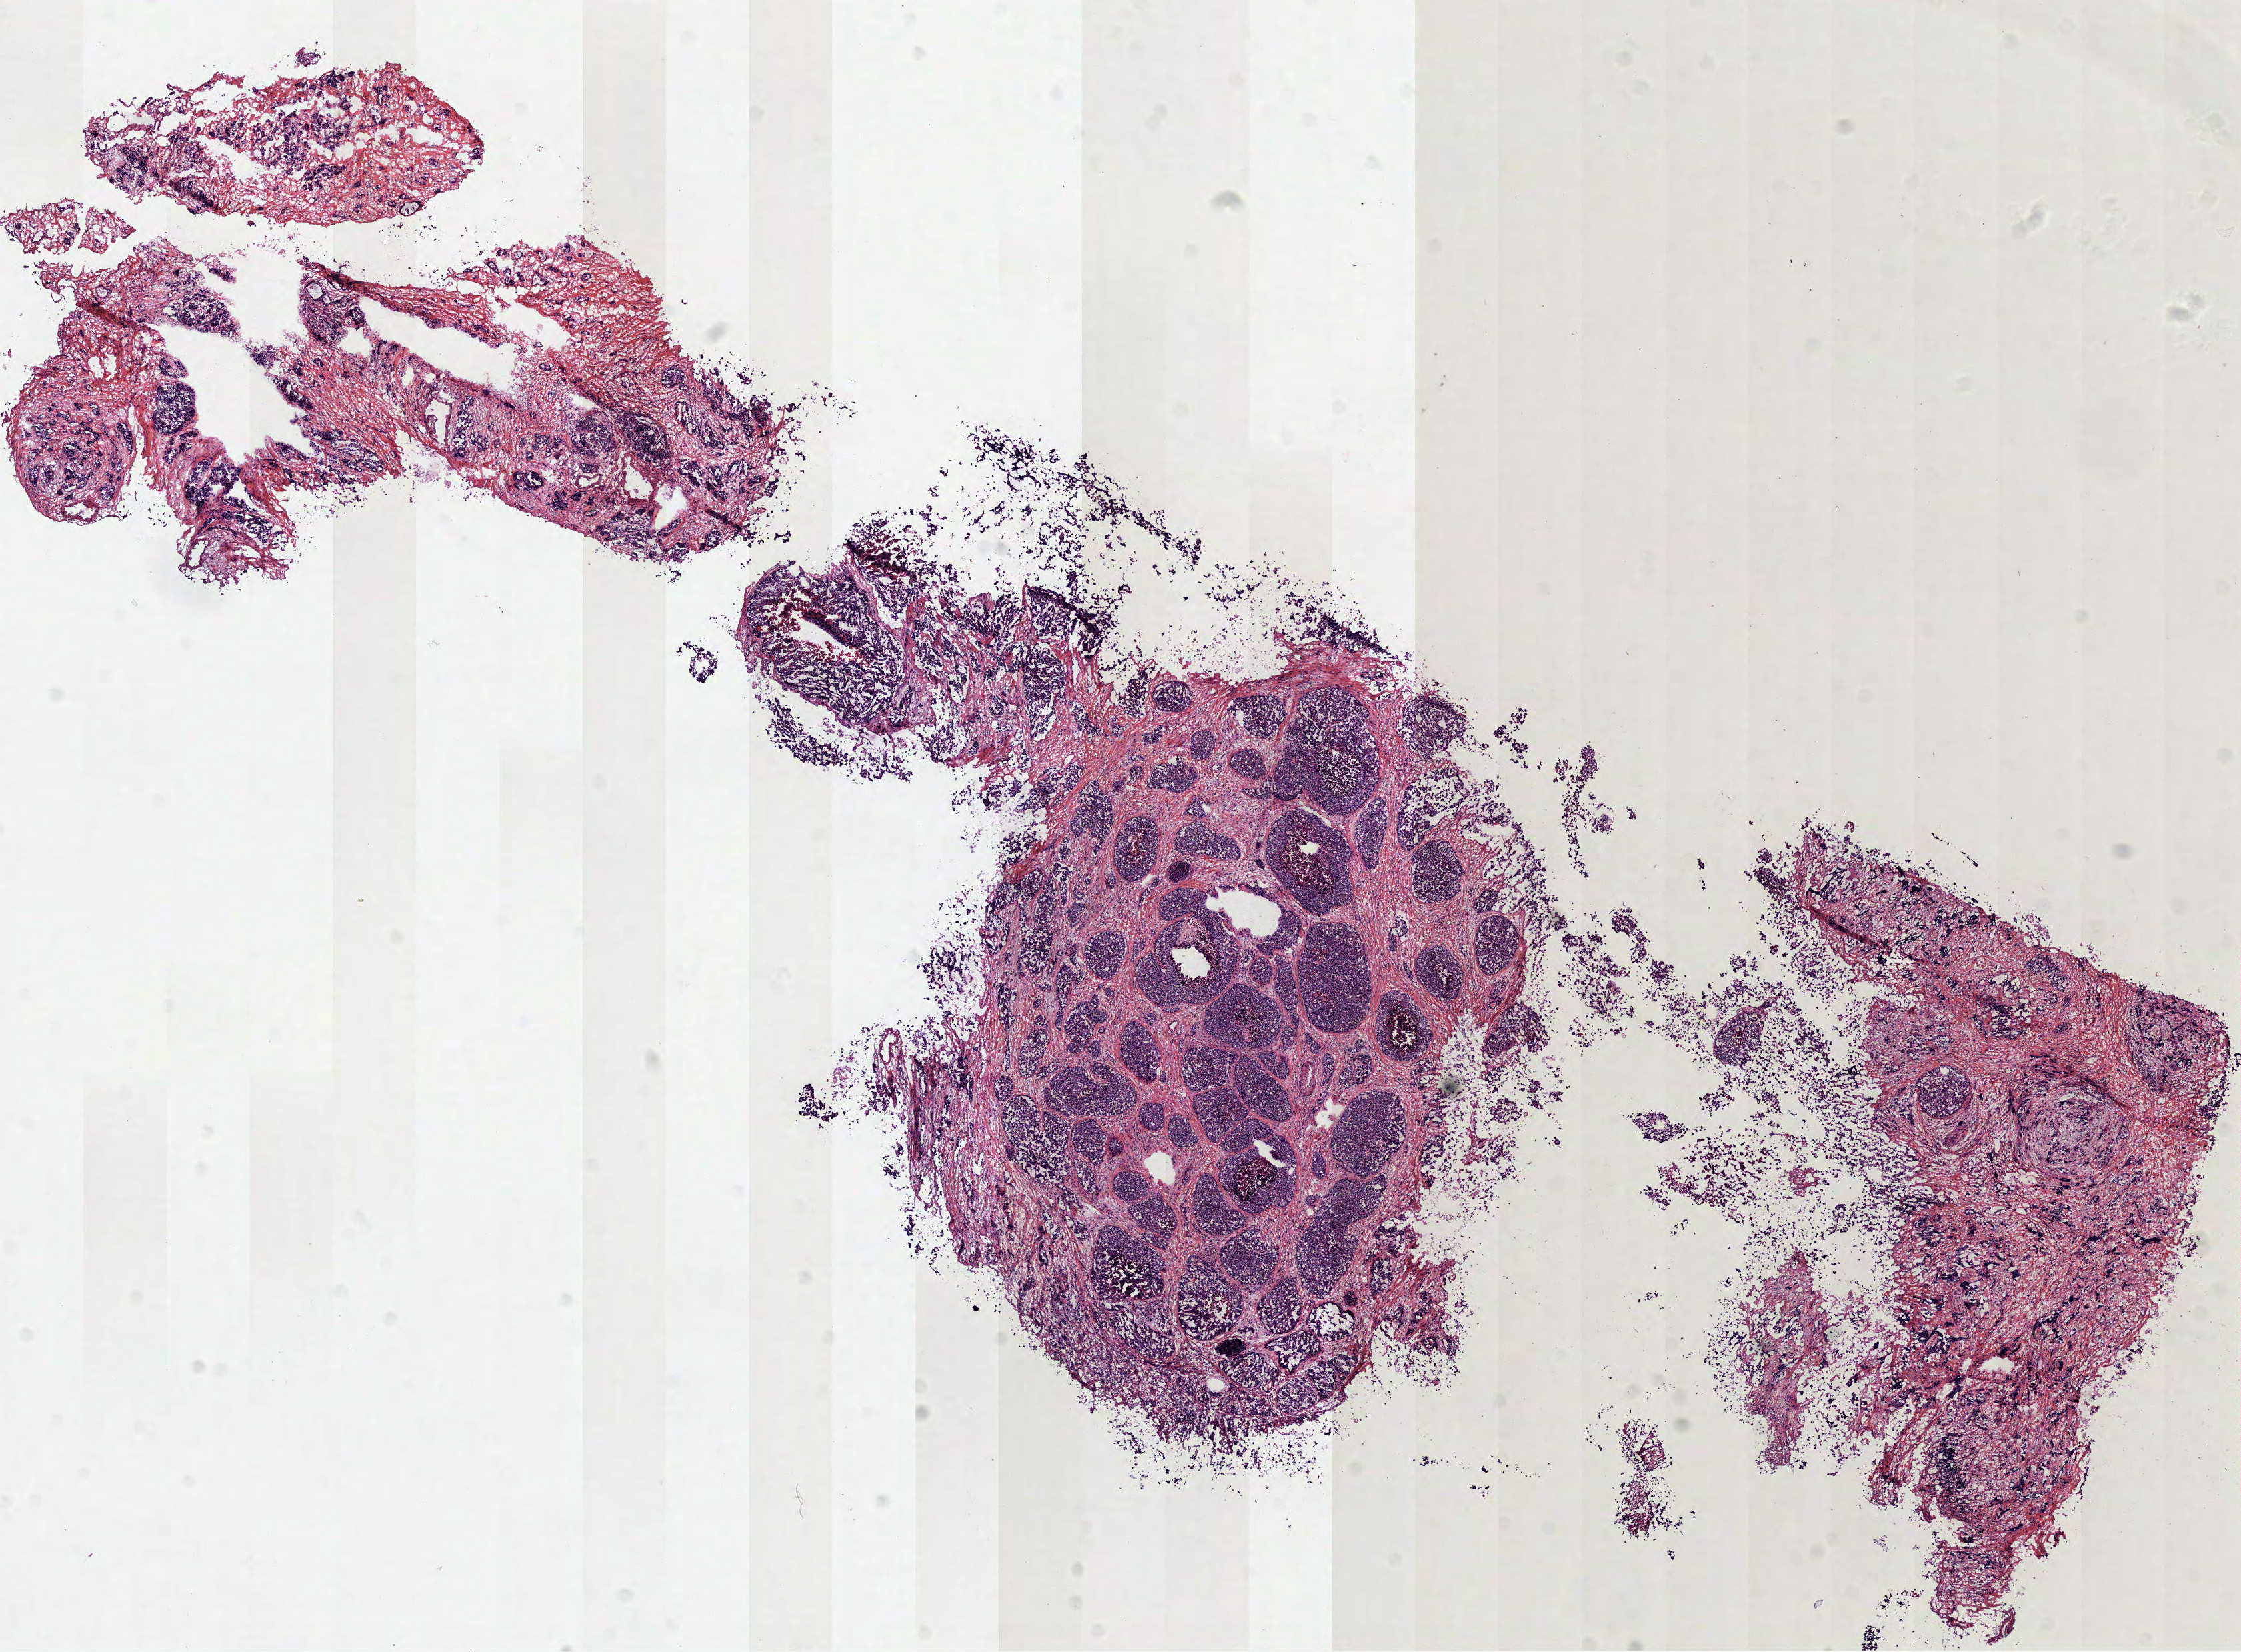
Whole-slide histology image, H&E — whole scanned area (about 13.6 x 10.0 mm, from a 40x scan) shown as a low-resolution overview. Frozen section. Primary tumour sample from the stomach. Patient: male, age at initial diagnosis 48 years. Histologic grade: G3 (poorly differentiated). Composition of this section per pathologist review: tumour cells 77%, tumour nuclei 90%, normal cells 0%, stromal cells 20%, necrosis 3%.
TNM: T3 N0 M0. Pathologic diagnosis: Adenocarcinoma, NOS. AJCC pathologic stage: II.